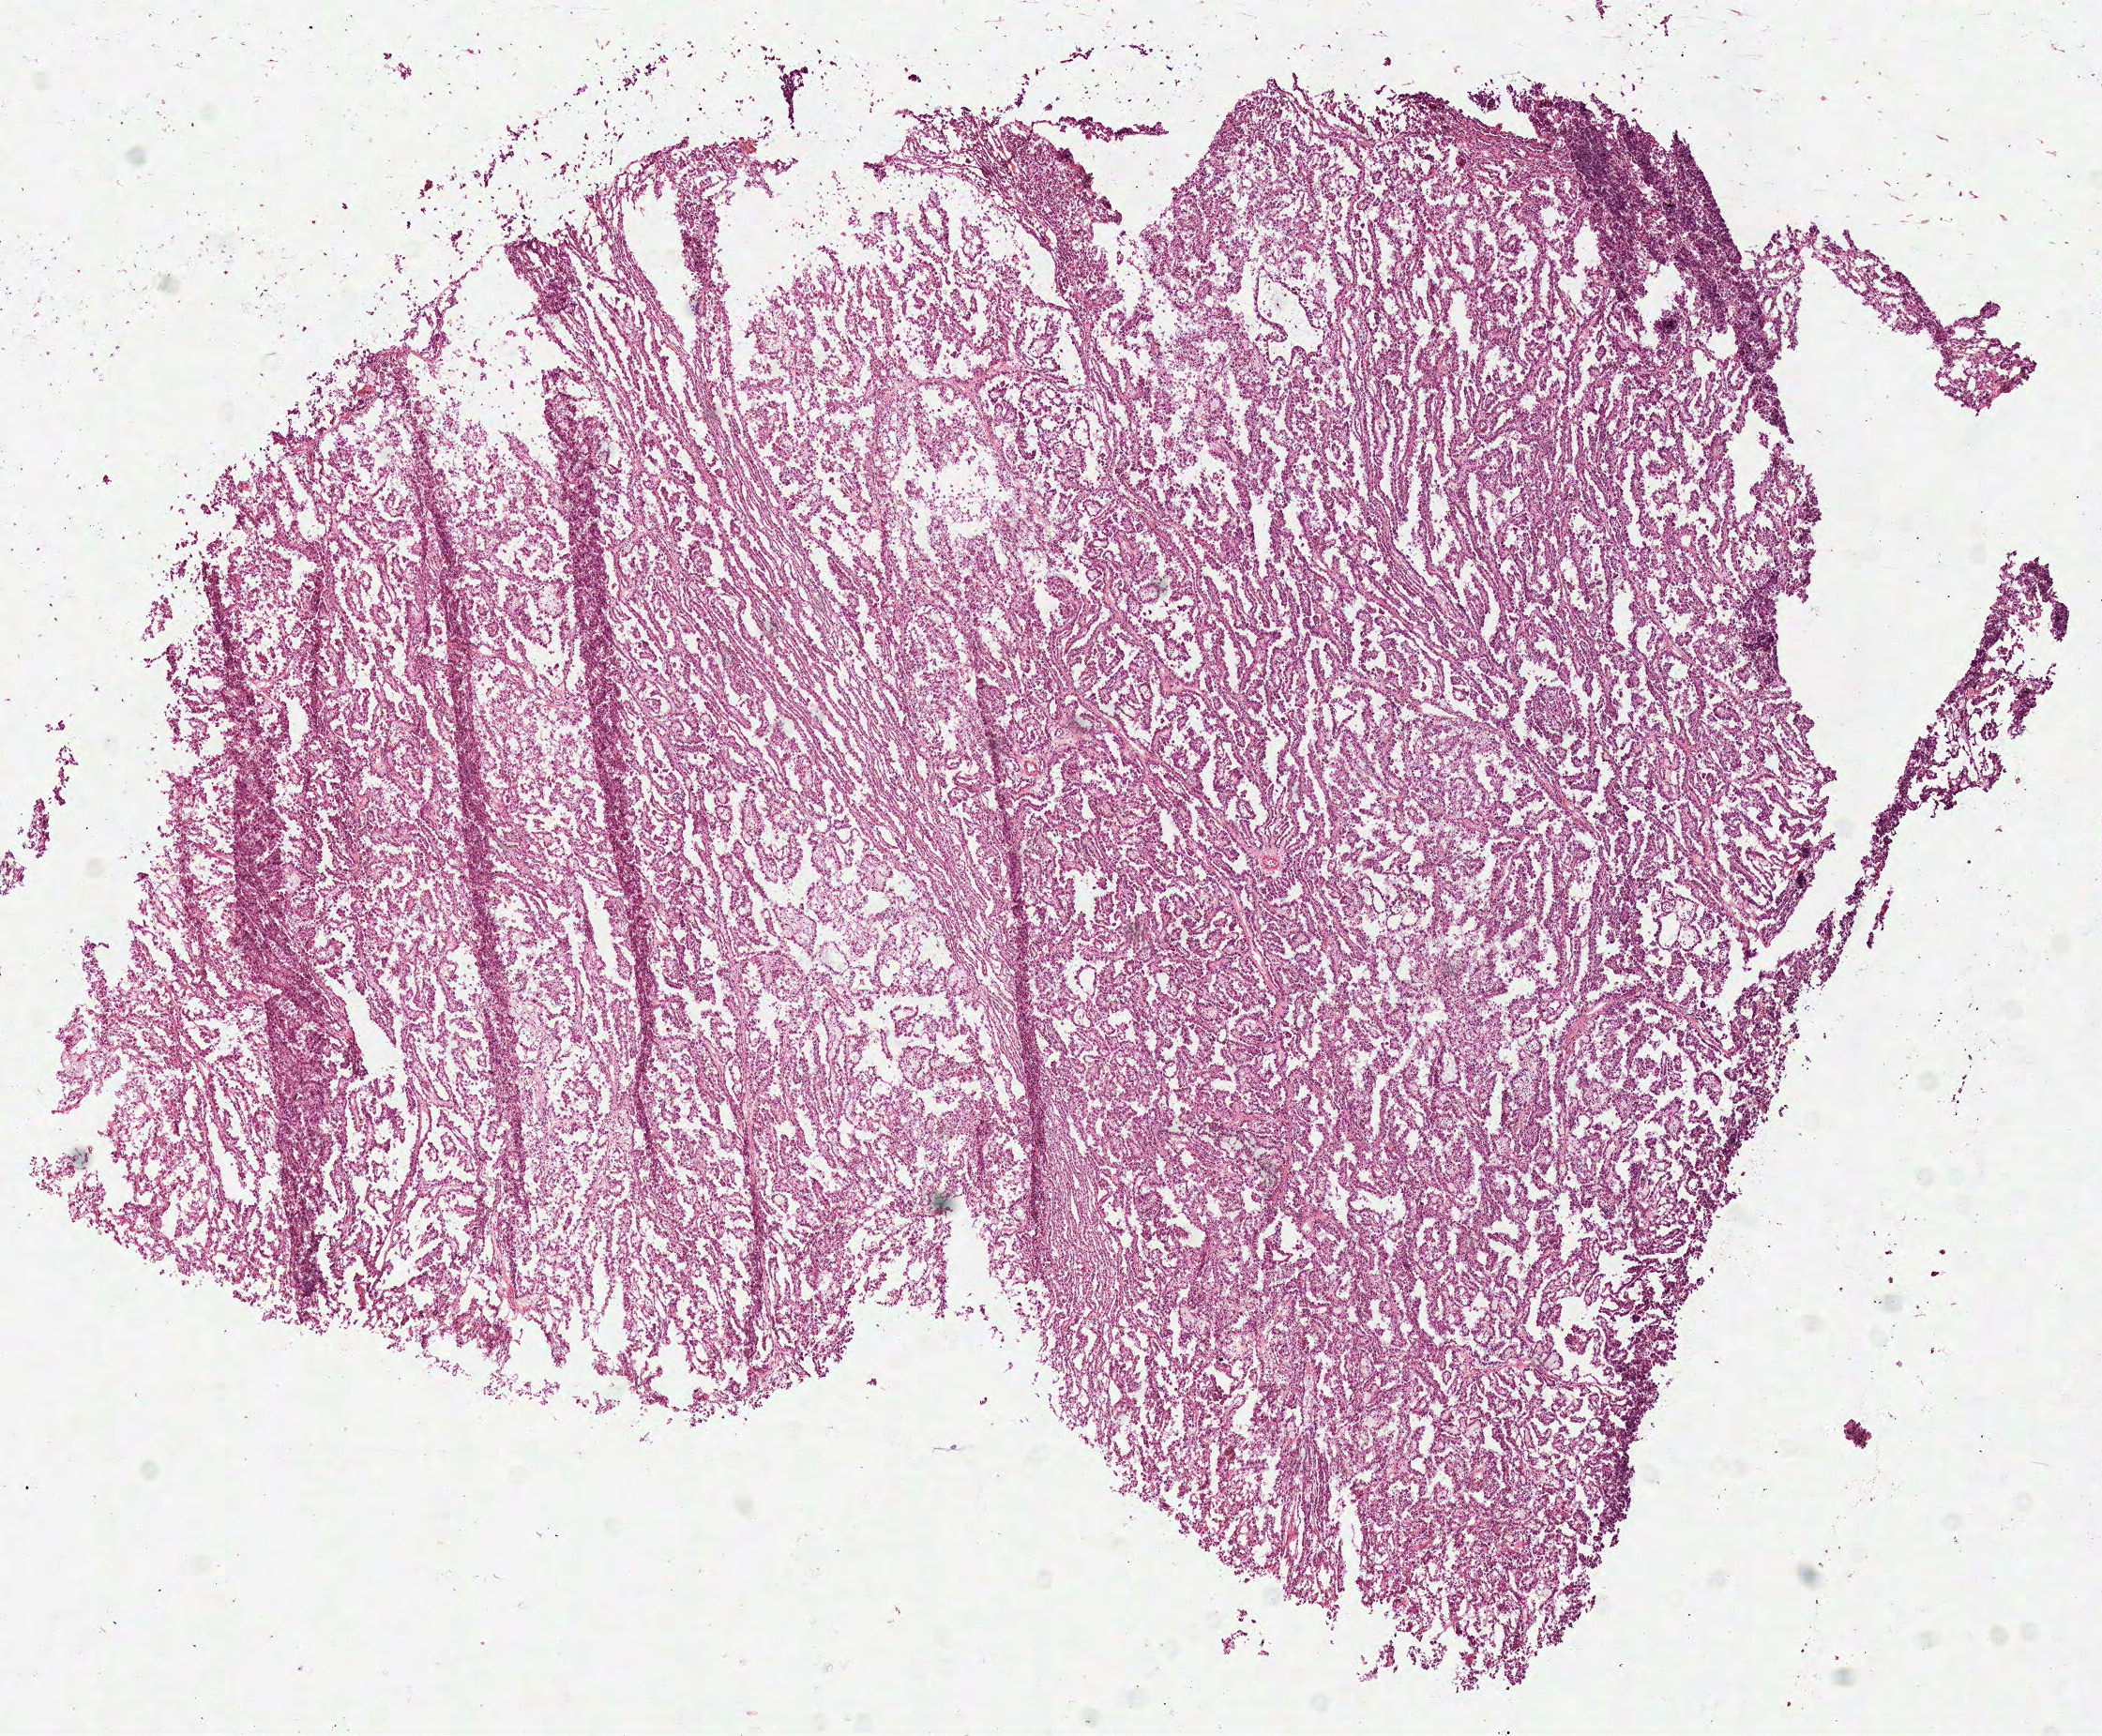
Digitized H&E tissue section (whole slide) — whole scanned area (about 8.8 x 7.3 mm, slide scanned at 40x) shown as a low-resolution overview, frozen section, sample: primary tumour, kidney. Patient: male, age at initial diagnosis 56 years. Pathologist review of this section (percent, as recorded): tumour cells 99%, tumour nuclei 85%, normal cells 0%, stromal cells 0%, necrosis 1%.
Laterality: left. AJCC pathologic stage: I (6th edition). Diagnosis: Papillary adenocarcinoma, NOS. Lymph nodes positive (case pathology): 0 of 2 examined.